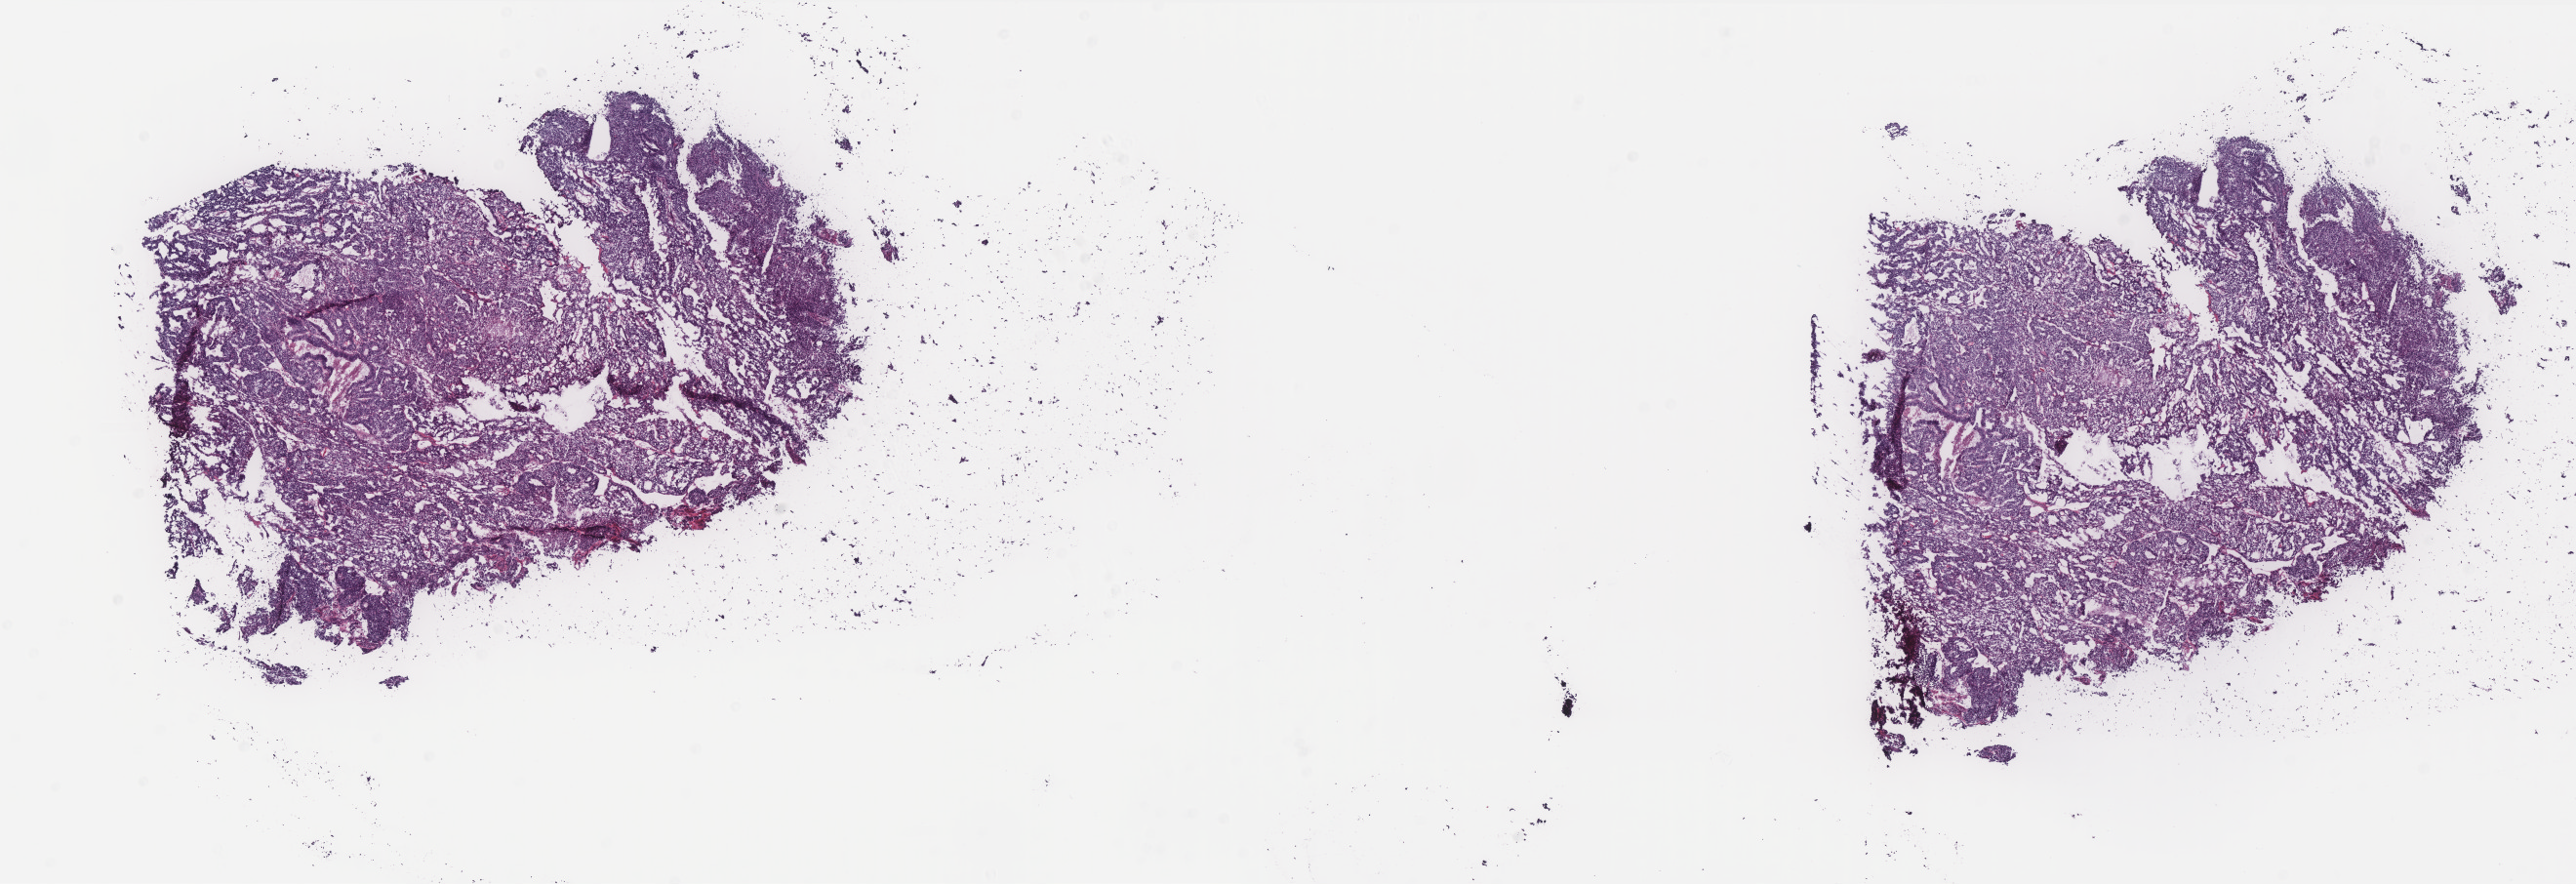
H&E whole-slide image — whole scanned area (about 21.2 x 7.3 mm, slide scanned at 40x) shown as a low-resolution overview. Frozen section. Sample: primary tumour, uterus. Patient sex: female. Histologic grade: G3 (poorly differentiated). Pathologist review of this section (percent, as recorded): tumour cells 90%, tumour nuclei 95%, normal cells 0%, stromal cells 5%, necrosis 5%. Inflammatory infiltration, as recorded: lymphocyte infiltration 8%, monocyte infiltration 2%, neutrophil infiltration 4%.
* pathologic diagnosis: Endometrioid adenocarcinoma, NOS
* FIGO stage: IB